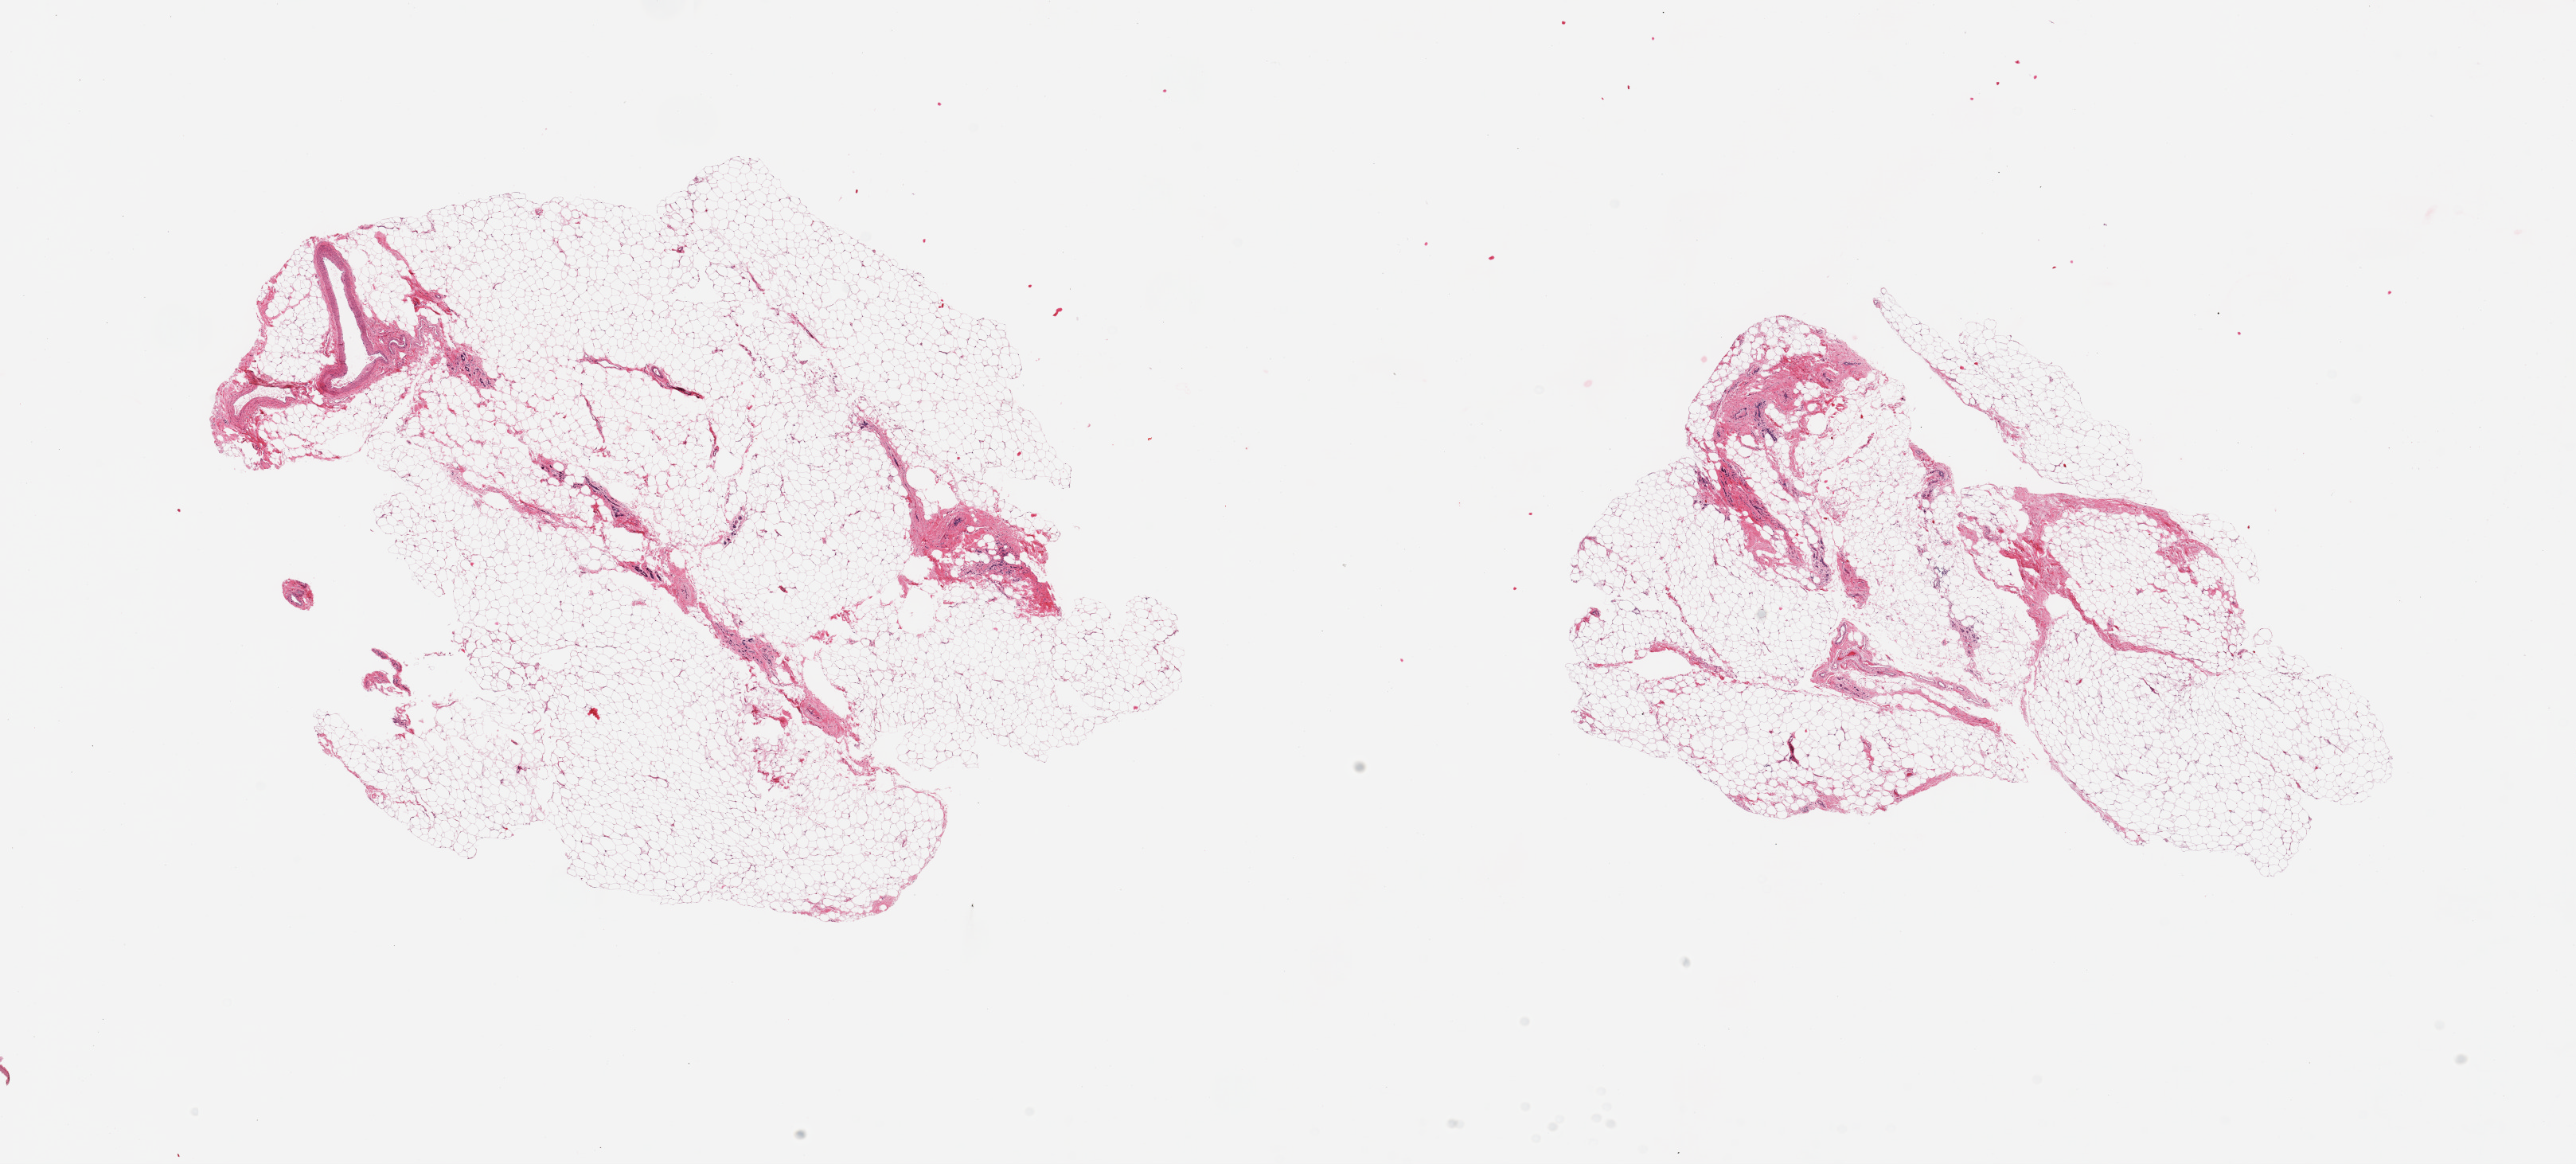
Digitized hematoxylin and eosin (H&E)-stained section, whole scanned area (about 25.6 x 11.6 mm, from a 20x scan) shown as a low-resolution overview, PAXgene-fixed paraffin-embedded (PFPE) section, sampled site (target tissue): breast, tissue donor sample. Donor sex: female.
* review note (as recorded): 2 pieces; atrophic ducts in fibrofatty tissue with 80% fat content